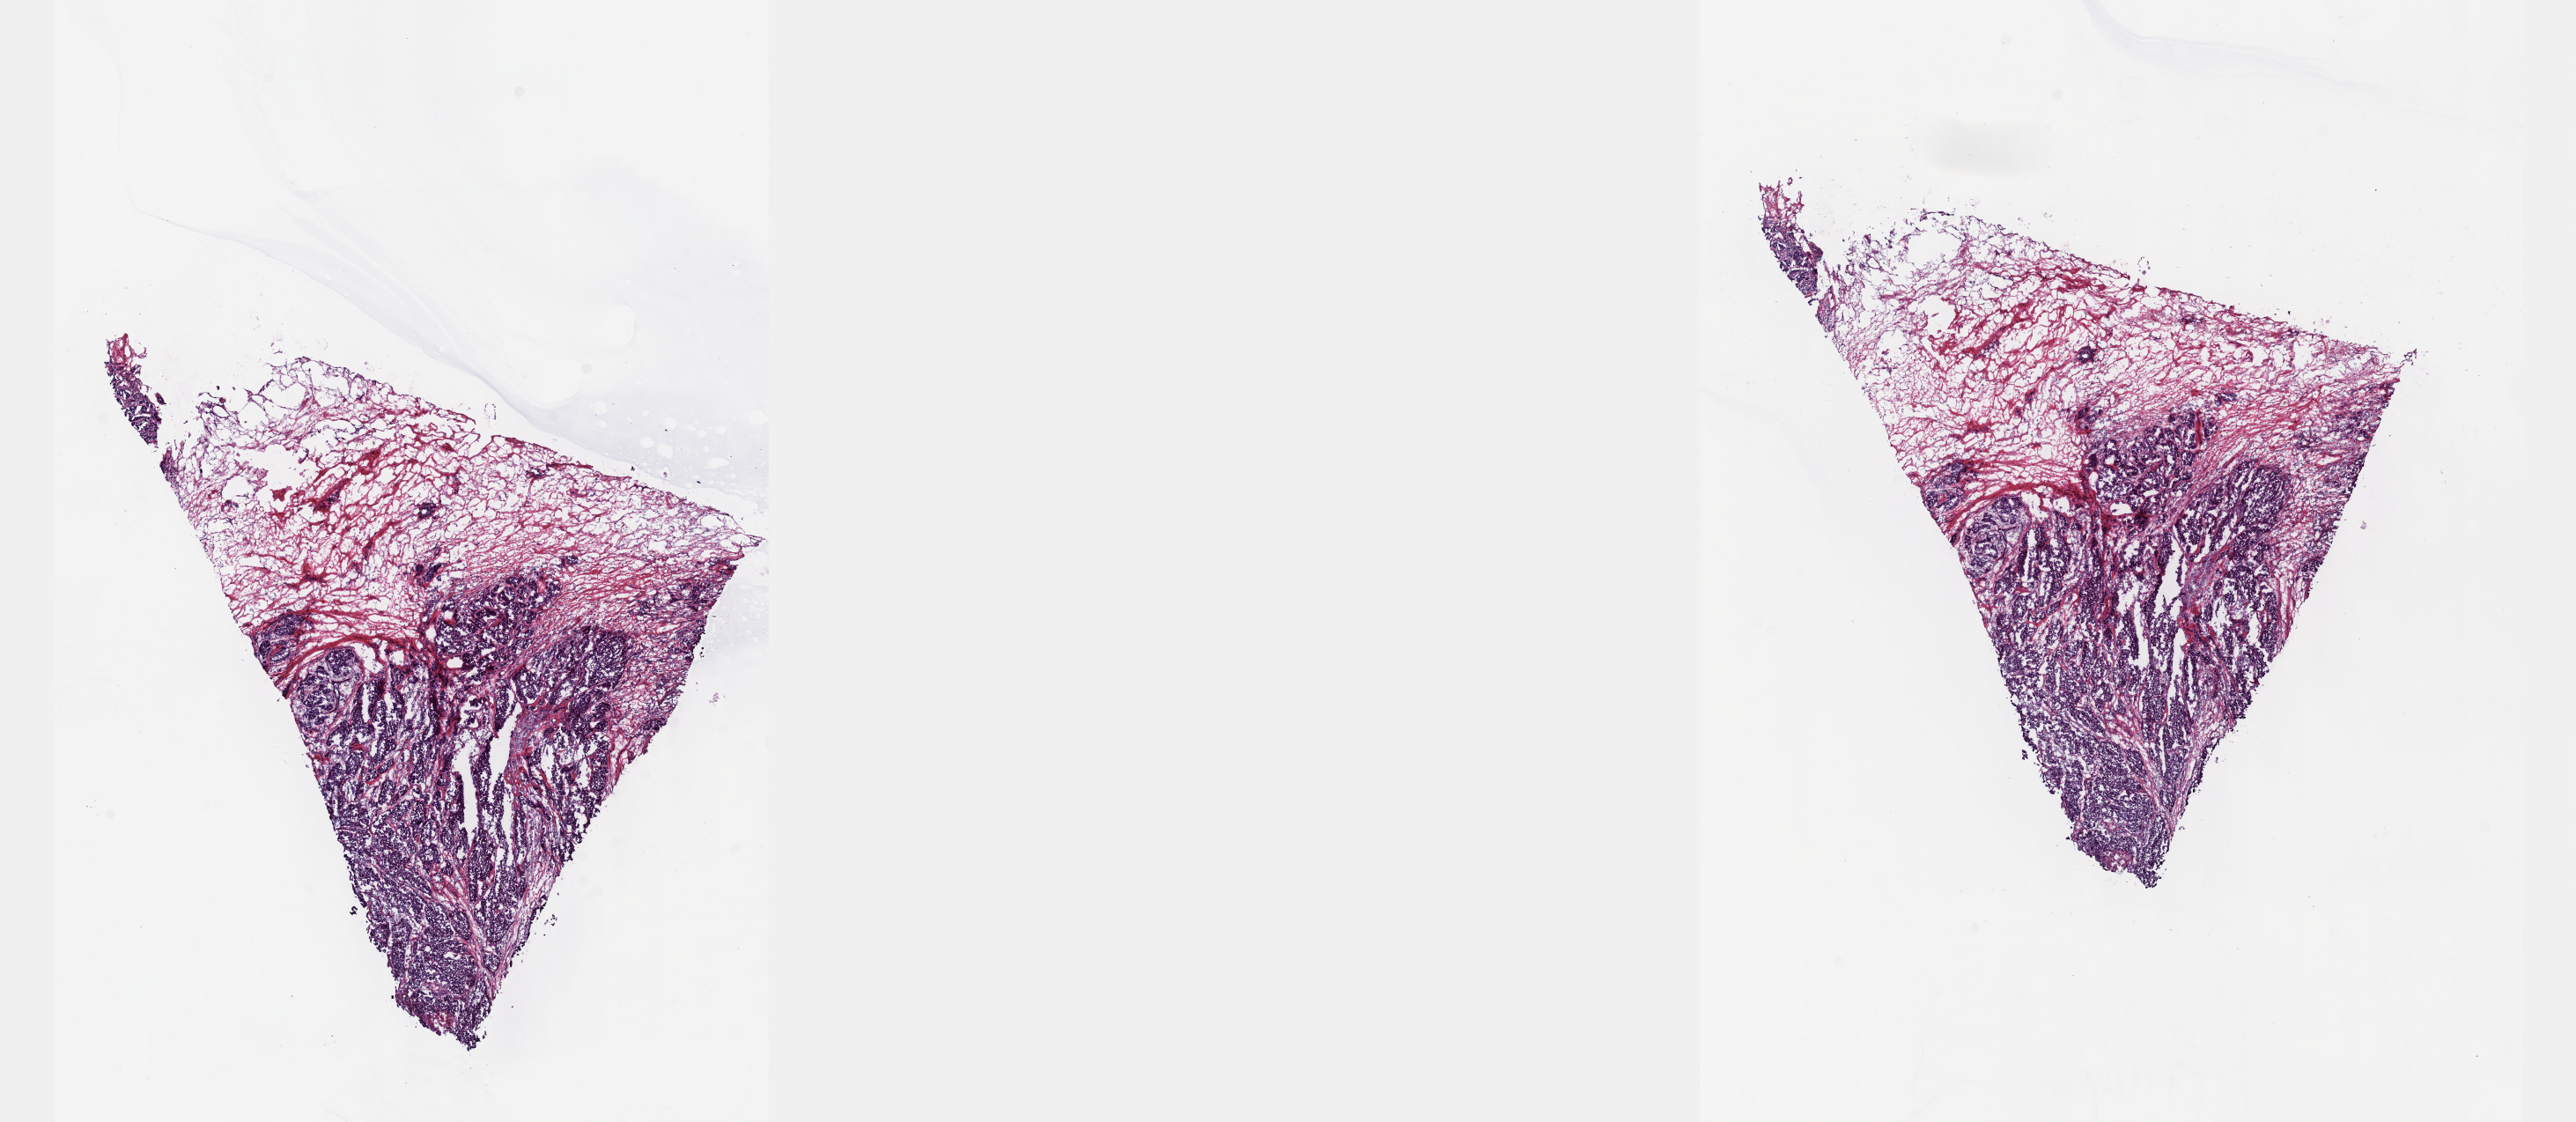
Whole-slide histology image, Hematoxylin and eosin (H&E) stained, shown as a low-resolution overview of the whole scanned area (about 23.6 x 10.3 mm, slide scanned at 40x). Frozen section from the top of the tissue portion. Breast, primary tumour sample. Female patient; age at initial diagnosis 63 years. Slide review estimates, as recorded: tumour cells 70%, tumour nuclei 80%, normal cells 10%, stromal cells 20%, necrosis 0%. Infiltration values recorded for this section: lymphocyte infiltration 0%, monocyte infiltration 0%, neutrophil infiltration 0%.
* histologic diagnosis: Infiltrating duct carcinoma, NOS
* laterality: right
* AJCC pathologic stage: IV (7th edition)